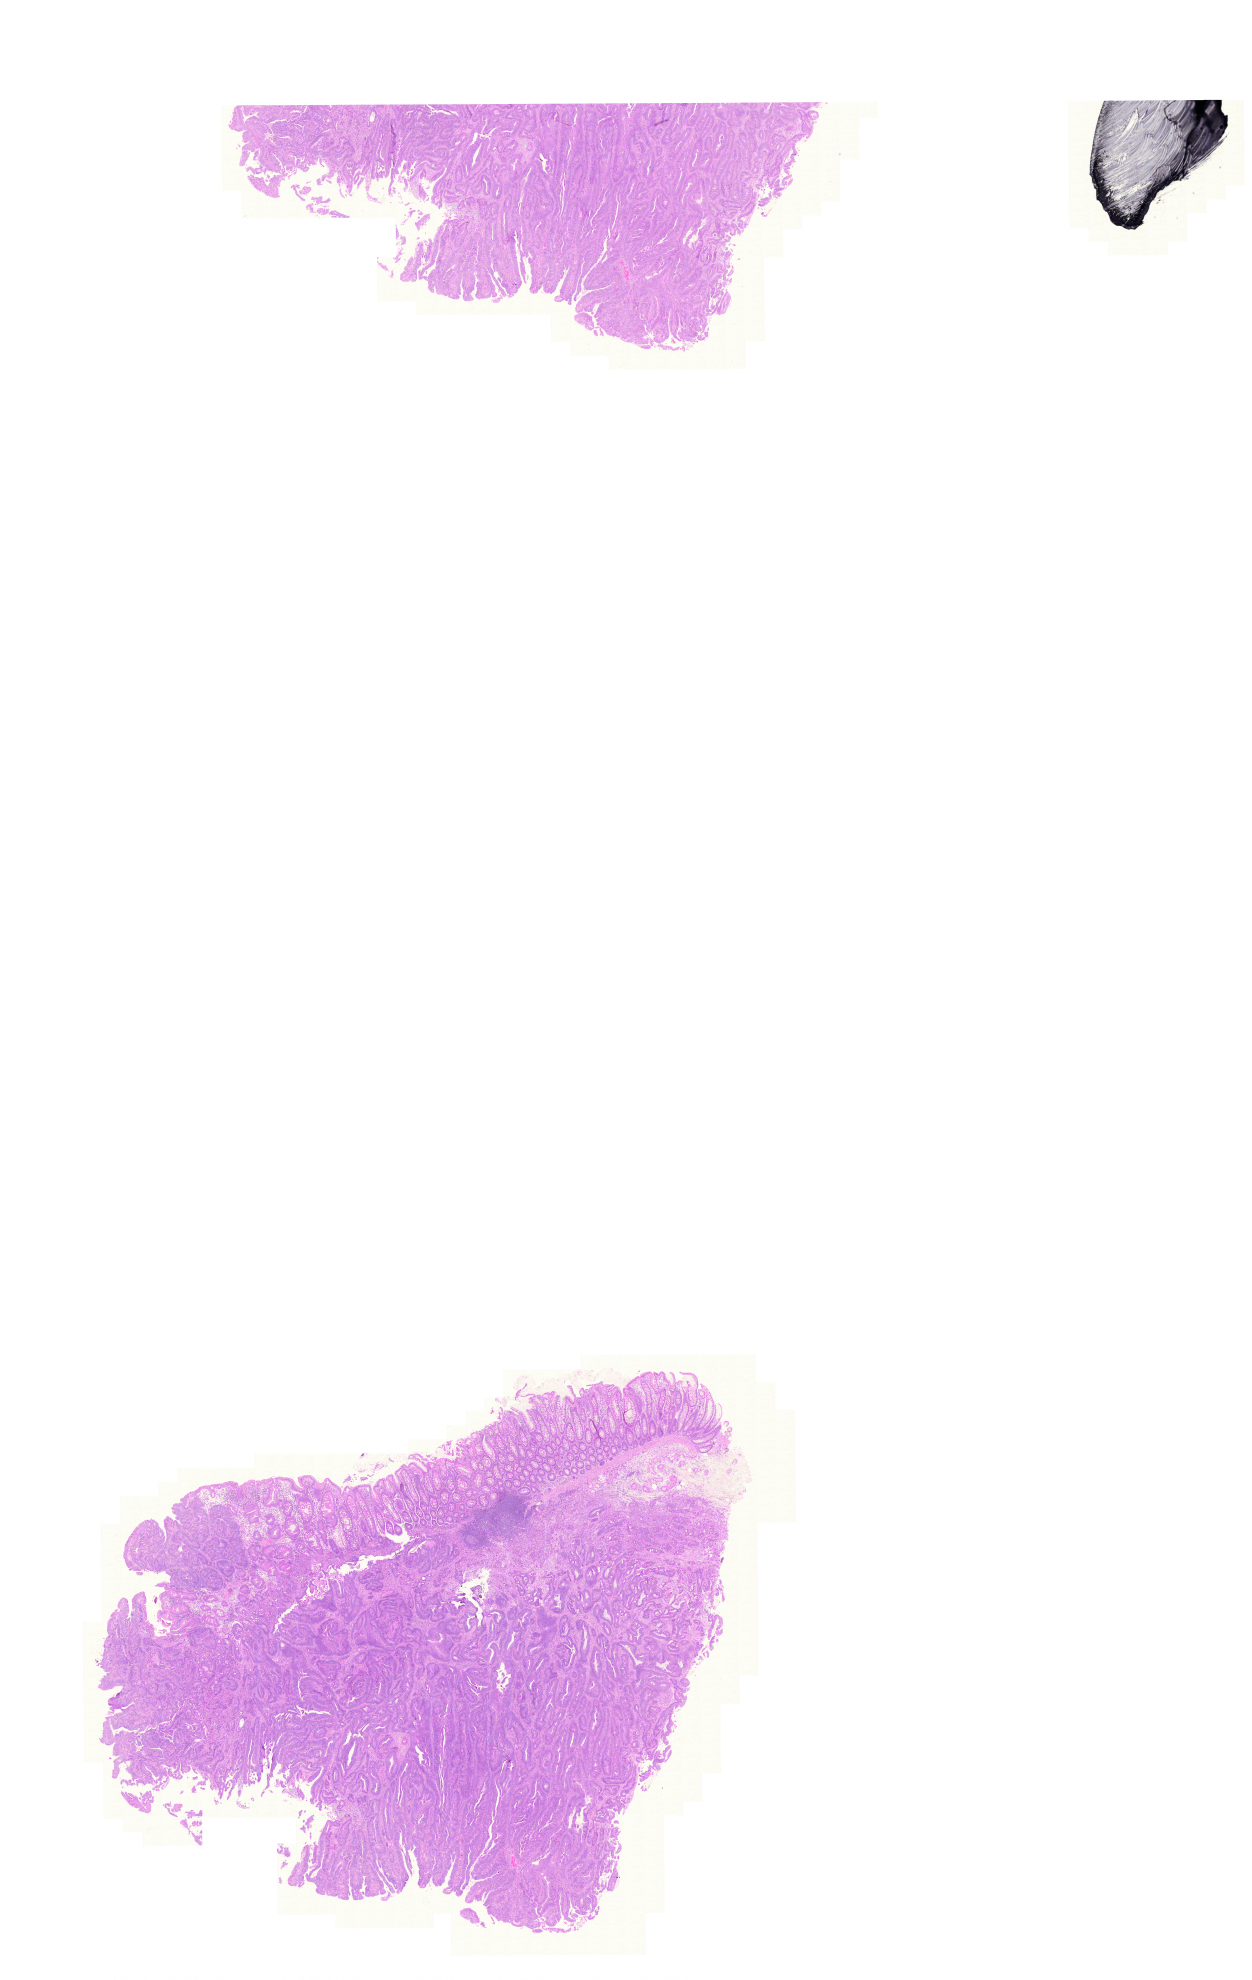
Whole-slide histology image, H&E, low-resolution overview of the scanned area, about 18.6 x 29.5 mm (acquisition: 20x scan). Formalin-fixed paraffin-embedded (FFPE) diagnostic section. Colon, primary tumour sample. Male, age 68 years at initial diagnosis.
* lymph nodes positive (case pathology): 0 of 12 examined
* diagnosis: Adenocarcinoma, NOS (ascending colon)
* AJCC pathologic stage: II